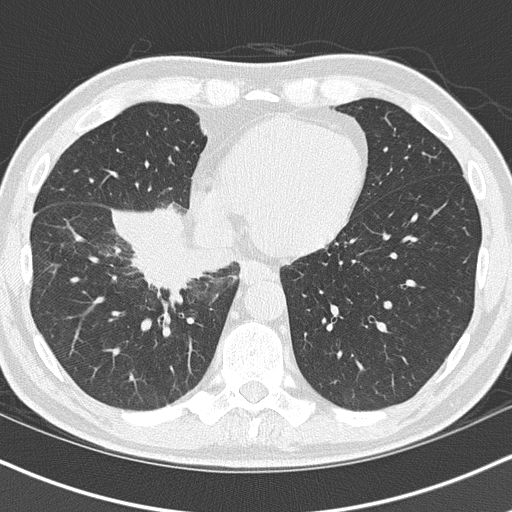
Chest CT (low-dose screening protocol), one axial image. Baseline screening round. Lung window (W 1500 / L -600 HU). 2 mm slice thickness. Lung (sharp) reconstruction kernel (B50f). Male participant, aged 55 years at enrolment. Current smoker at enrolment.
Expert-annotated lung lesion, bounding box <120,222,244,316> (left, top, right, bottom; pixels). Screening reader's record for this exam (one nodule recorded; not confirmed to be the boxed lesion): non-calcified nodule or mass ≥4 mm, right lower lobe, 6 × 5 mm, spiculated (stellate) margins, soft tissue attenuation. Participant outcome: lung cancer diagnosed 21 days after this screen — carcinoma, NOS, right hilum, stage IB (AJCC 6th edition), 67 mm at pathology.